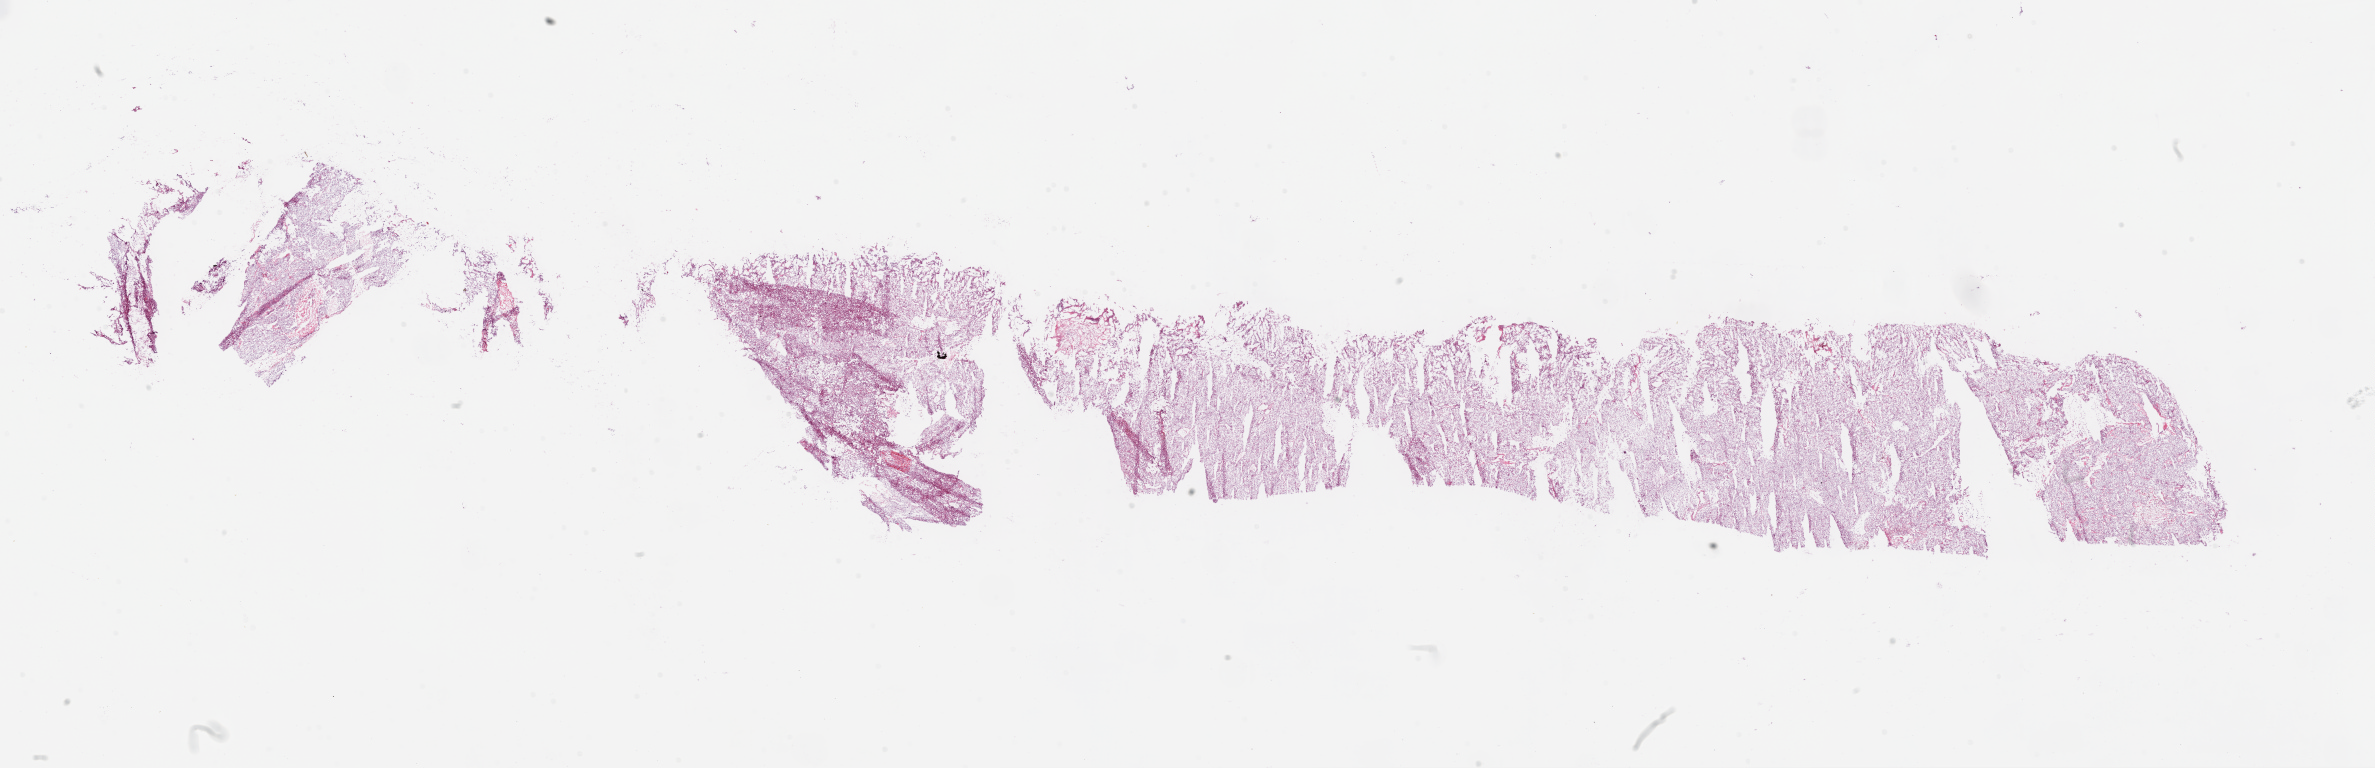
Hematoxylin and eosin (H&E) stained whole-slide image, a low-resolution overview of the entire scanned area, about 38.1 x 12.3 mm (acquisition: 20x scan), frozen section from the bottom of the tissue portion, primary tumour sample from the kidney. Male, age 48 years at initial diagnosis. Histologic grade: G3 (poorly differentiated). Pathologist review of this section (percent, as recorded): tumour cells 90%, tumour nuclei 85%, normal cells 0%, stromal cells 10%, necrosis 0%.
• pathologic diagnosis: Clear cell adenocarcinoma, NOS
• AJCC pathologic stage: I